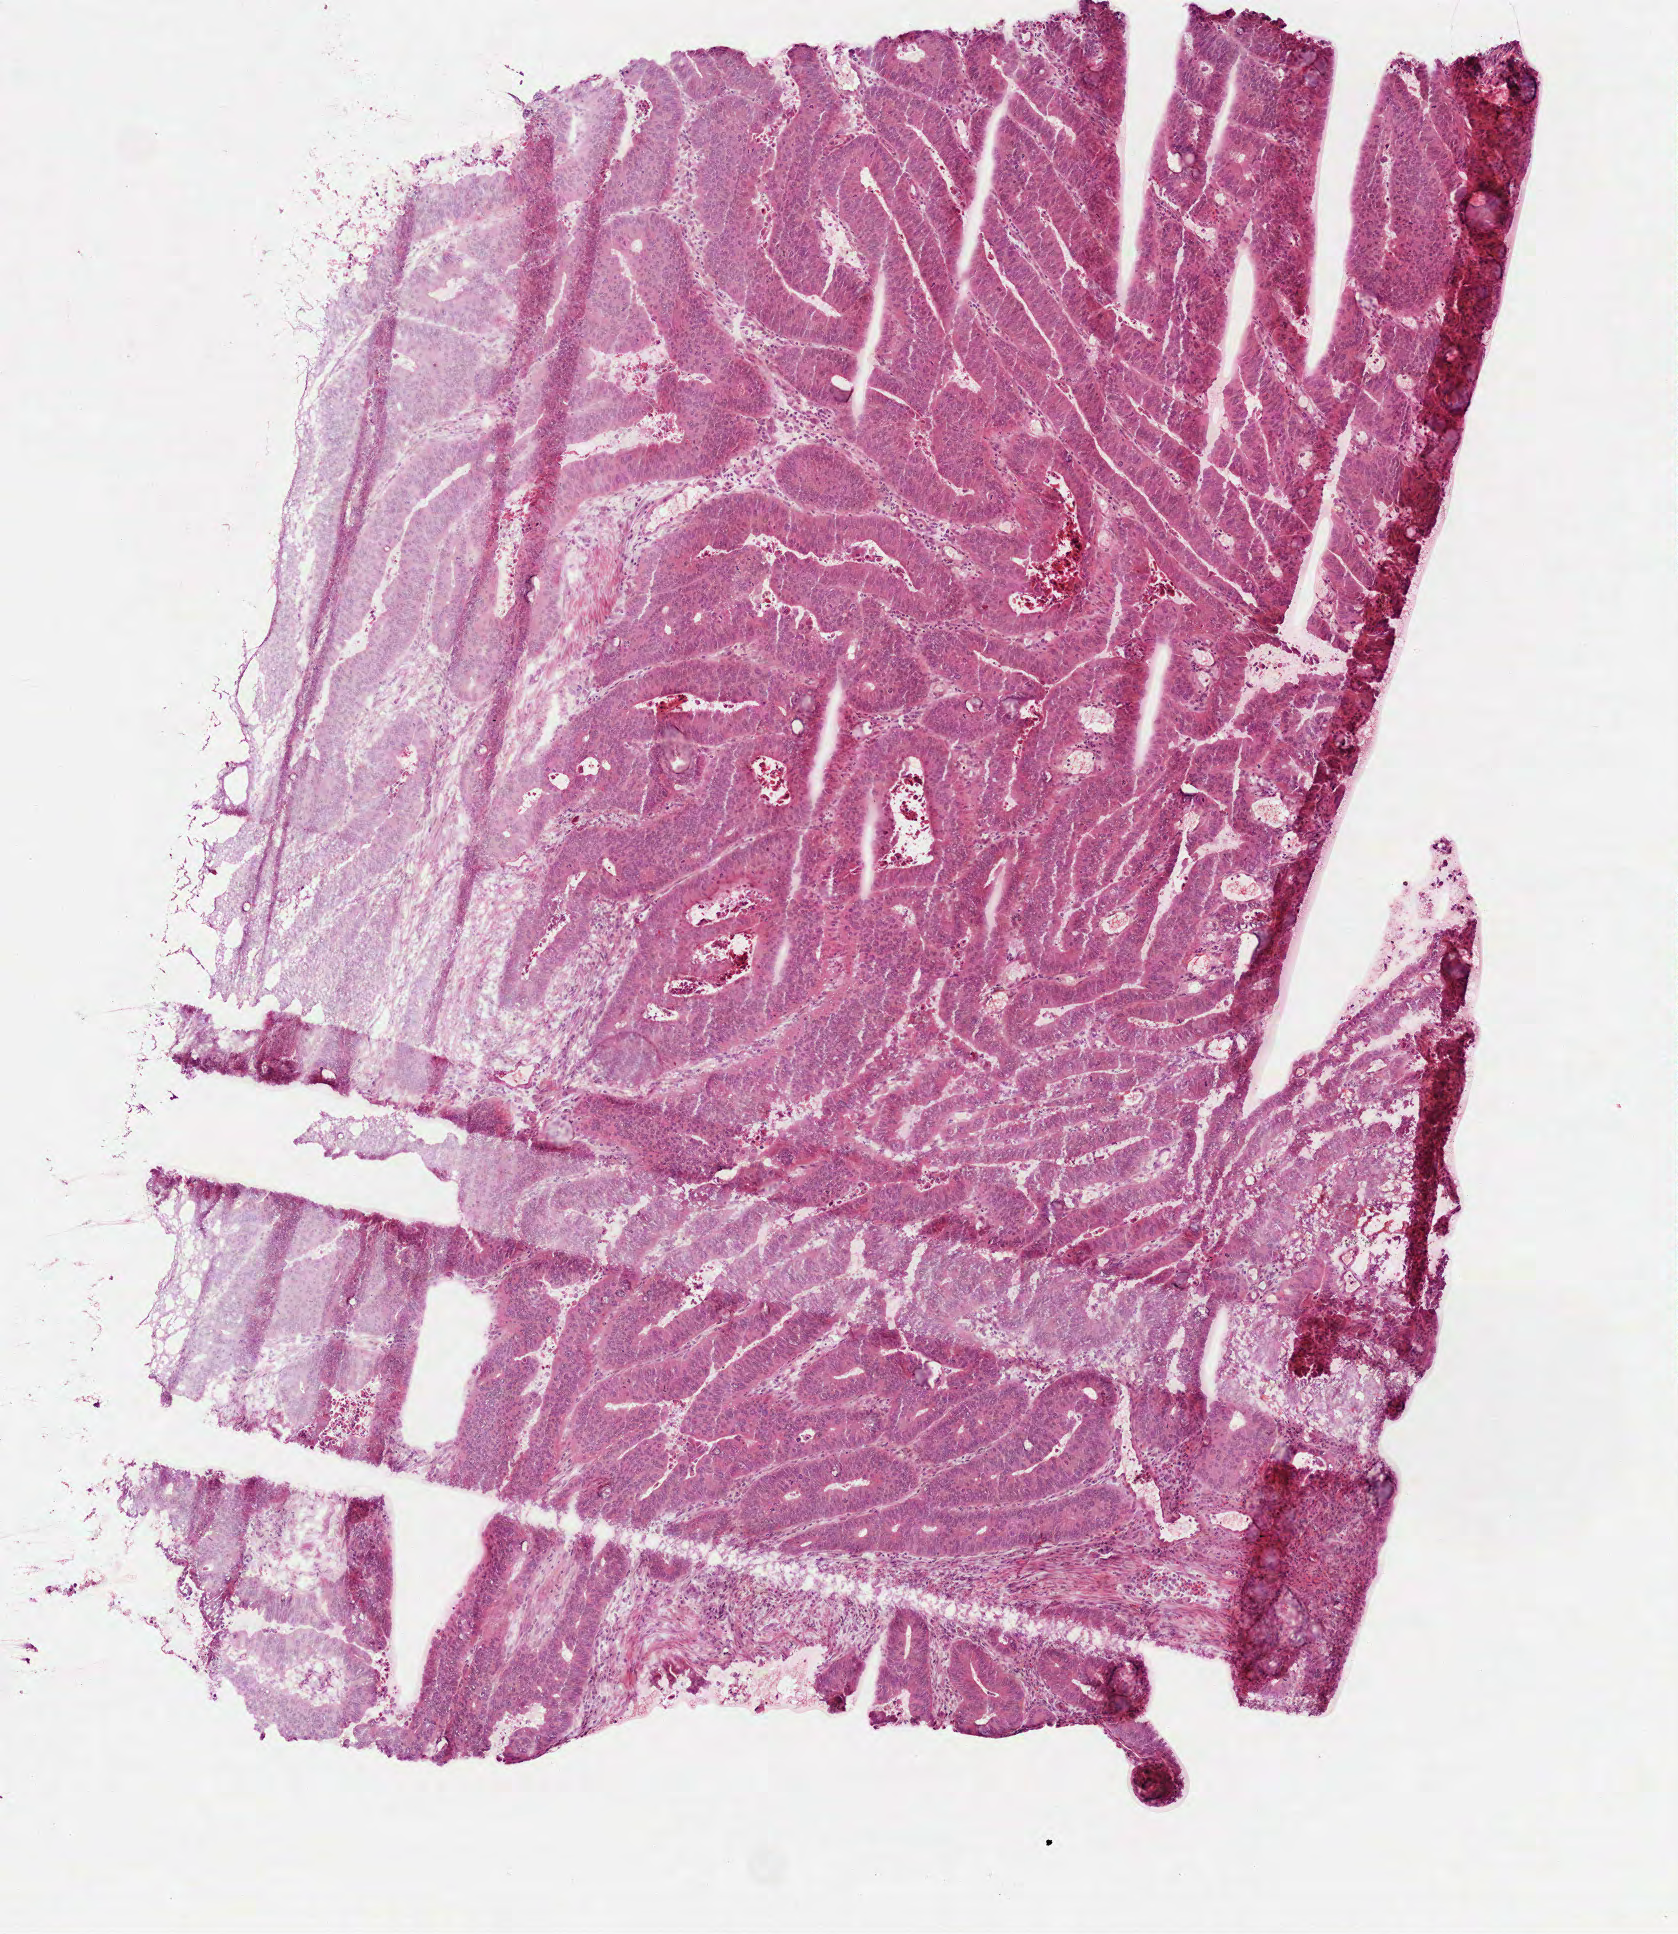
Digitized Hematoxylin and eosin (H&E) stained tissue section (whole slide) — low-resolution overview of the scanned area, about 3.4 x 3.9 mm (slide scanned at 40x); frozen section; primary tumour sample from the rectum. Male patient; age at initial diagnosis 60 years. Slide review estimates, as recorded: tumour cells 90%, tumour nuclei 85%, normal cells 0%, stromal cells 5%, necrosis 5%.
- lymph nodes positive (case pathology): 1 of 18 examined
- AJCC pathologic stage: IIIA (6th edition)
- histologic diagnosis: Adenocarcinoma in tubulovillous adenoma